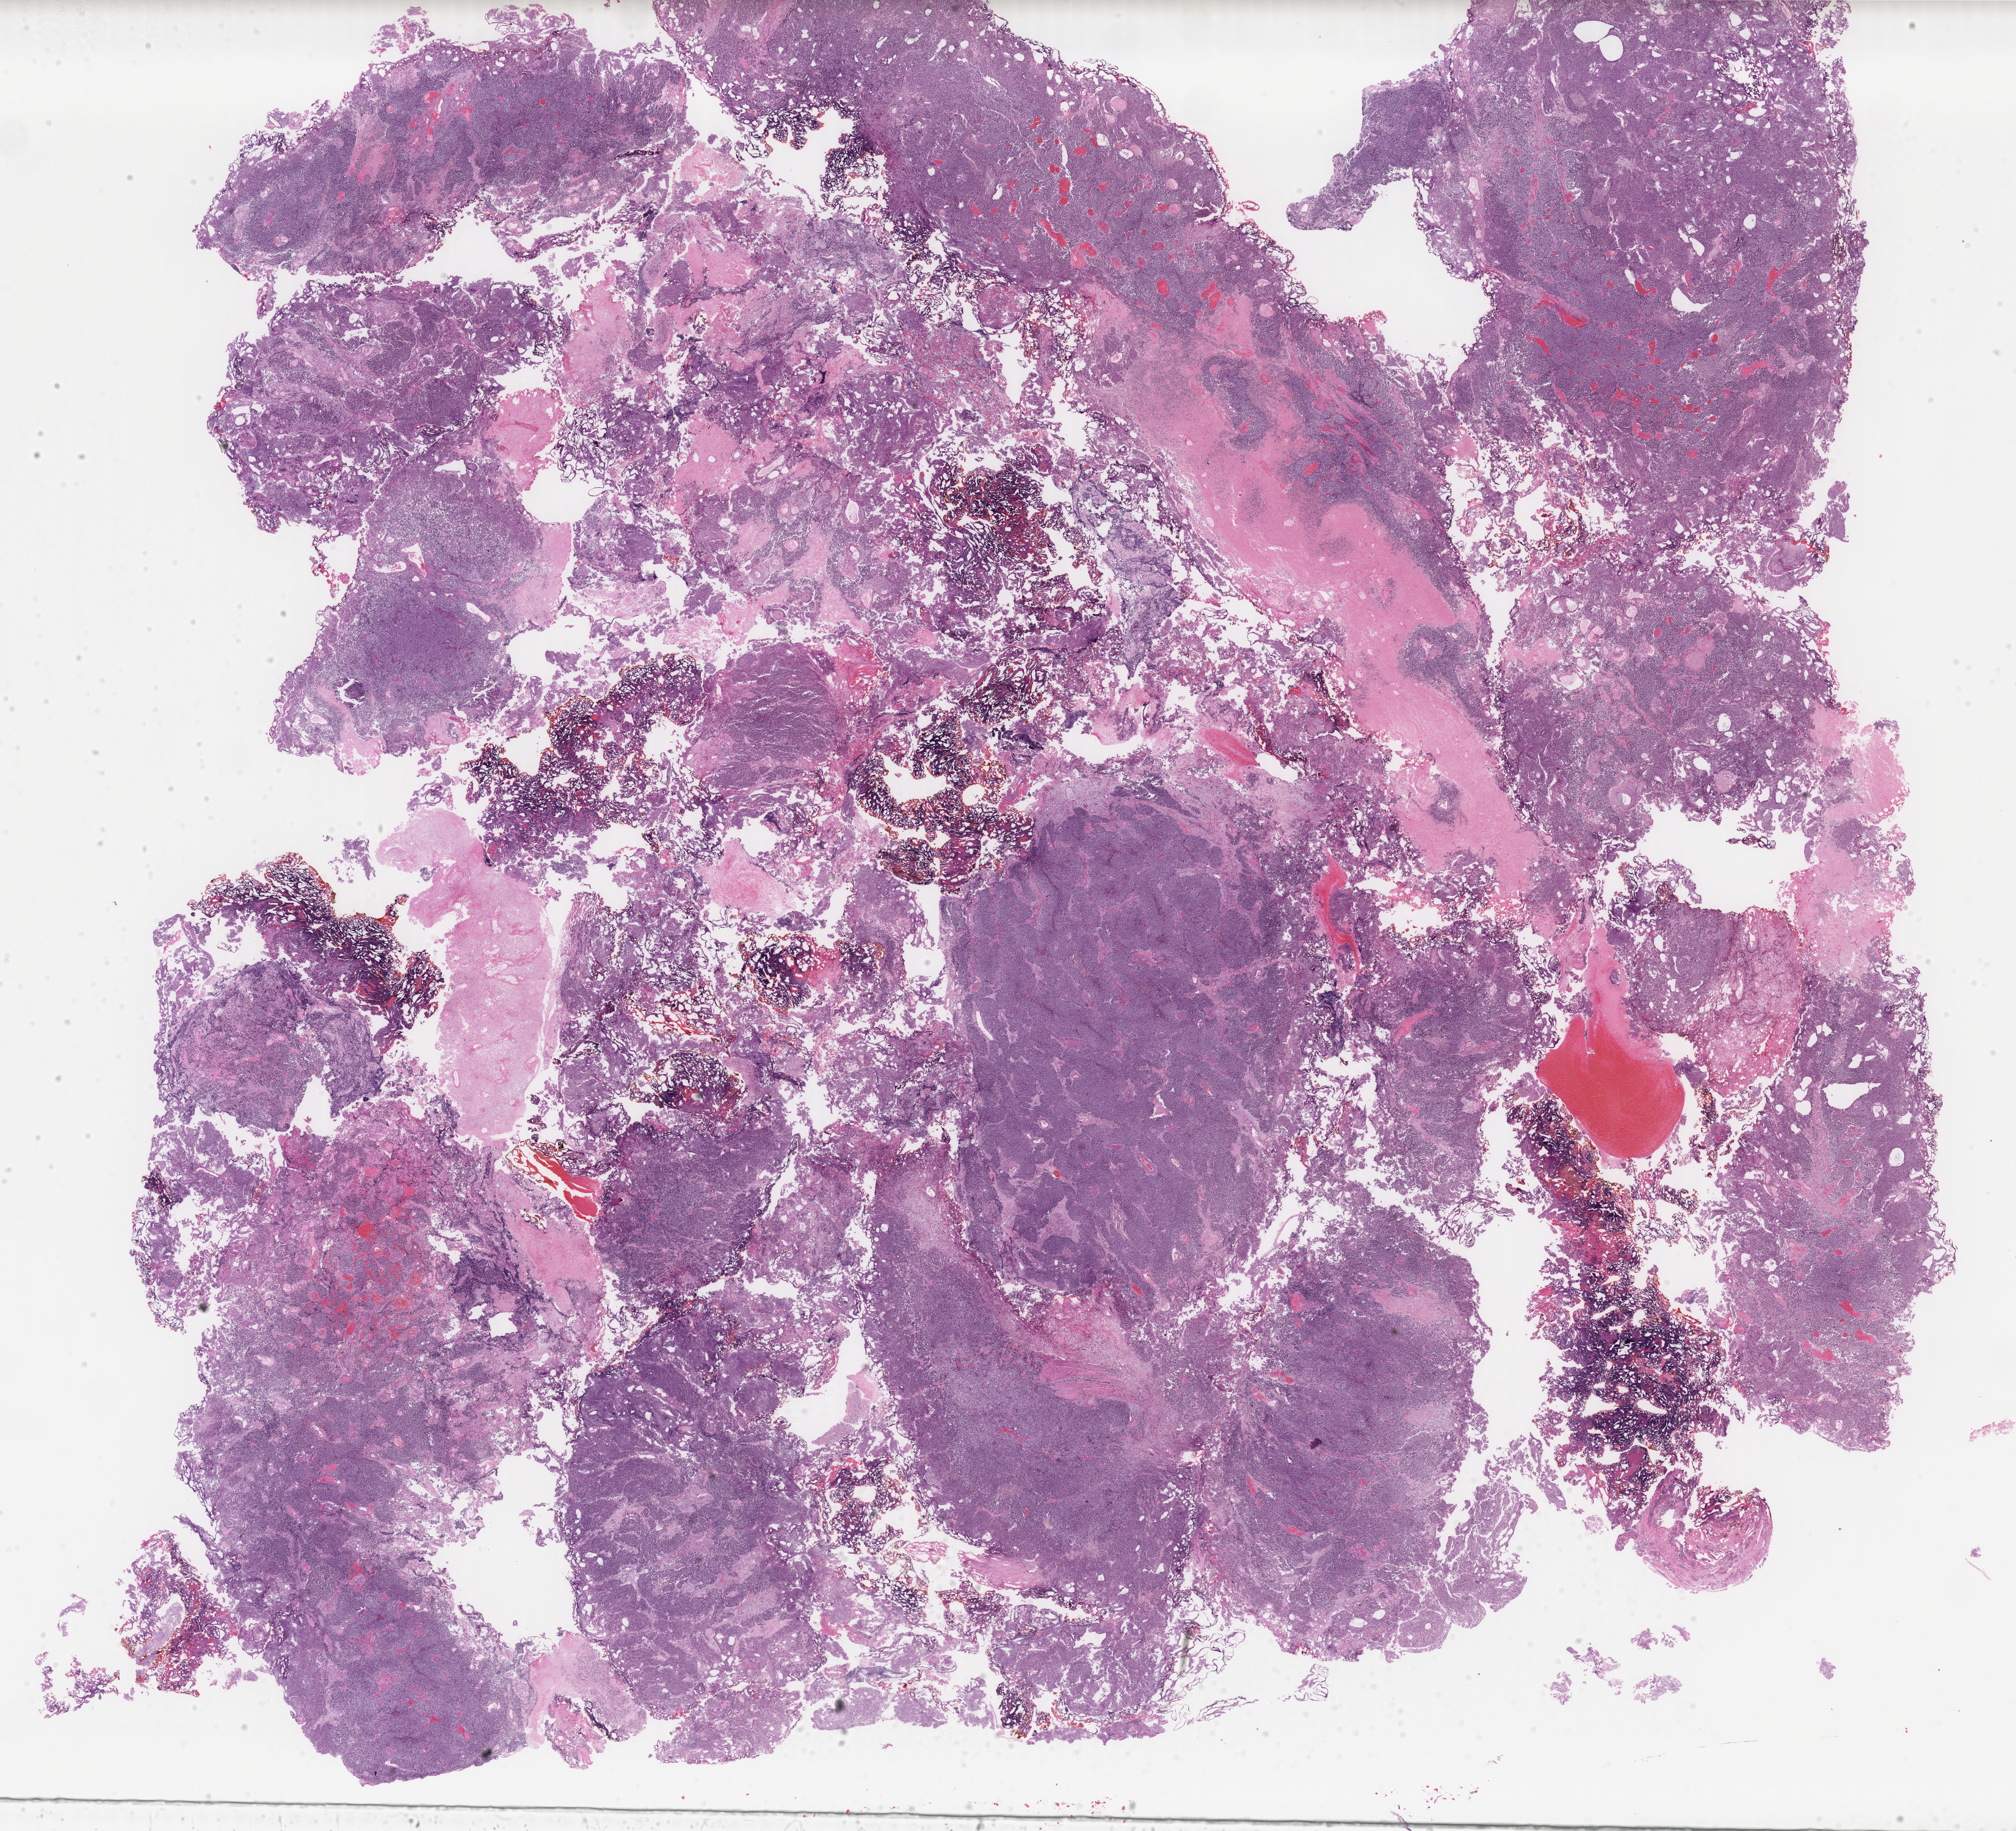
Digitized H&E tissue section (whole slide), low-resolution overview of the scanned area, about 26.2 x 23.8 mm (acquisition: 40x scan), FFPE section, bladder, primary tumour sample. Male, age 77 years at initial diagnosis.
Diagnosis: Transitional cell carcinoma (lateral wall of bladder).